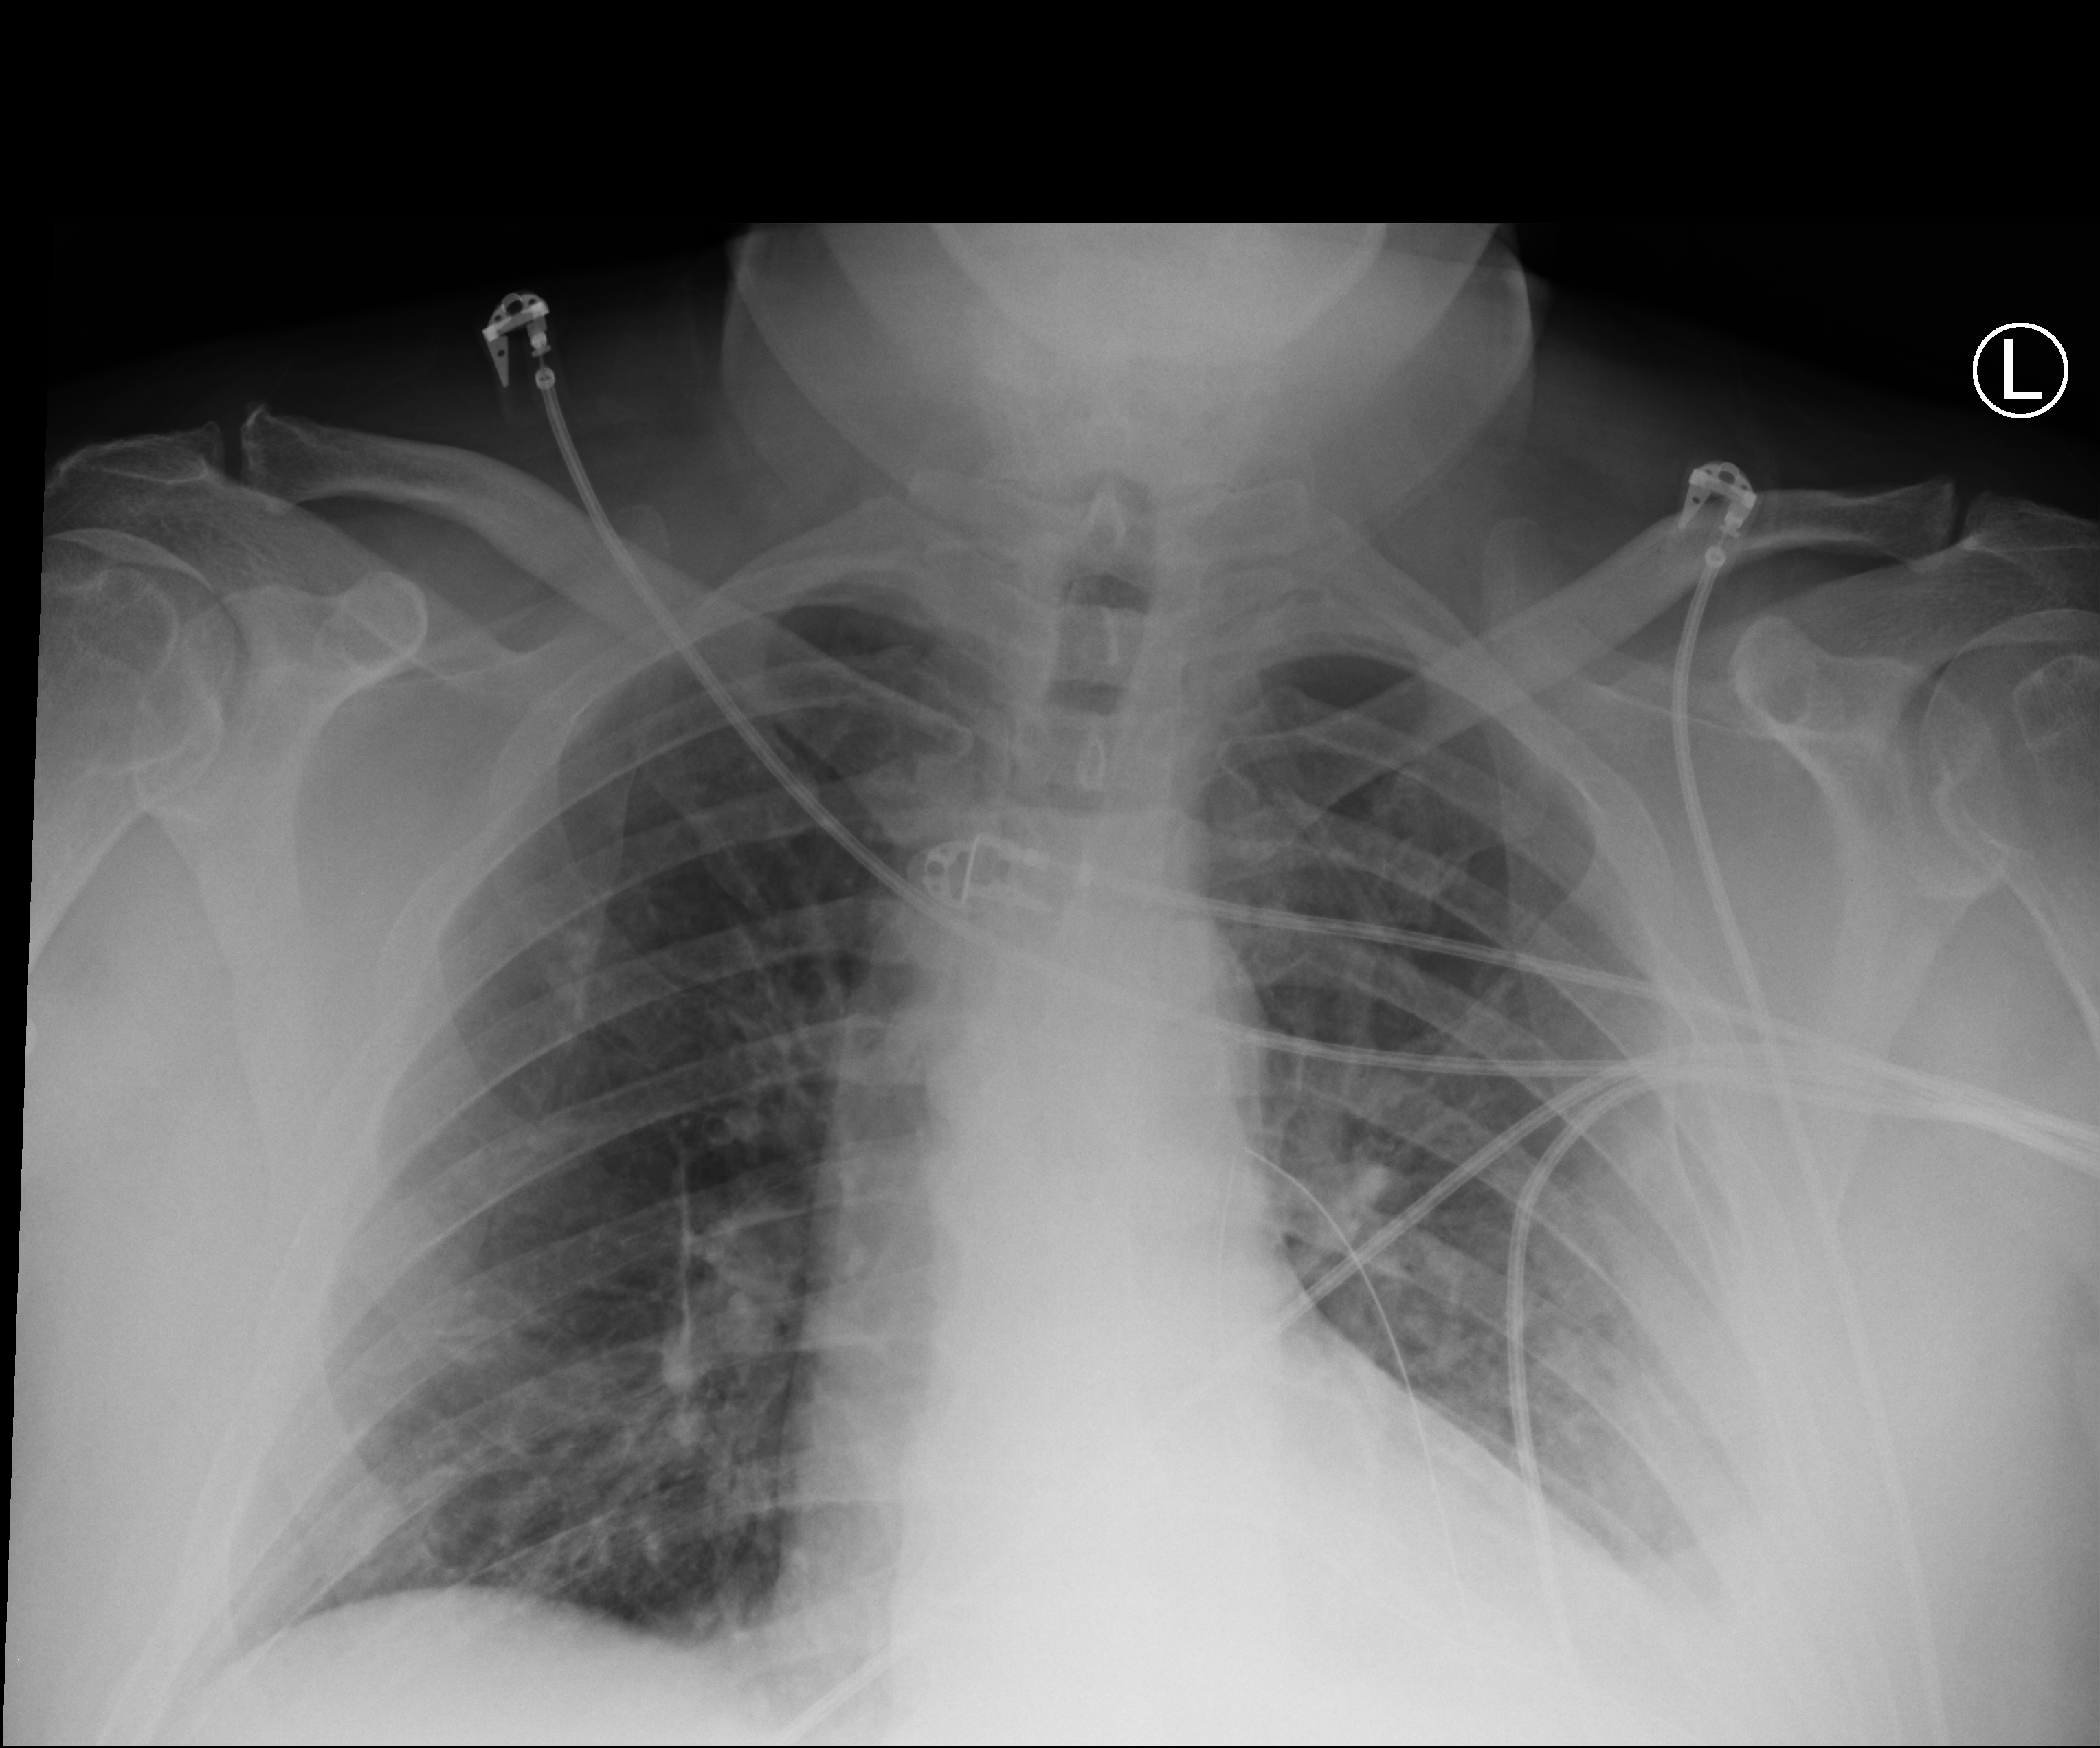
Portable chest radiograph, anteroposterior (AP) projection. Patient hospitalised with COVID-19; male, aged 18–59 years.
Admission-level facts for this patient (not findings on this image; timing relative to this image not recorded): mechanically ventilated during this hospital stay: no; admitted to intensive care during this hospital stay: no.